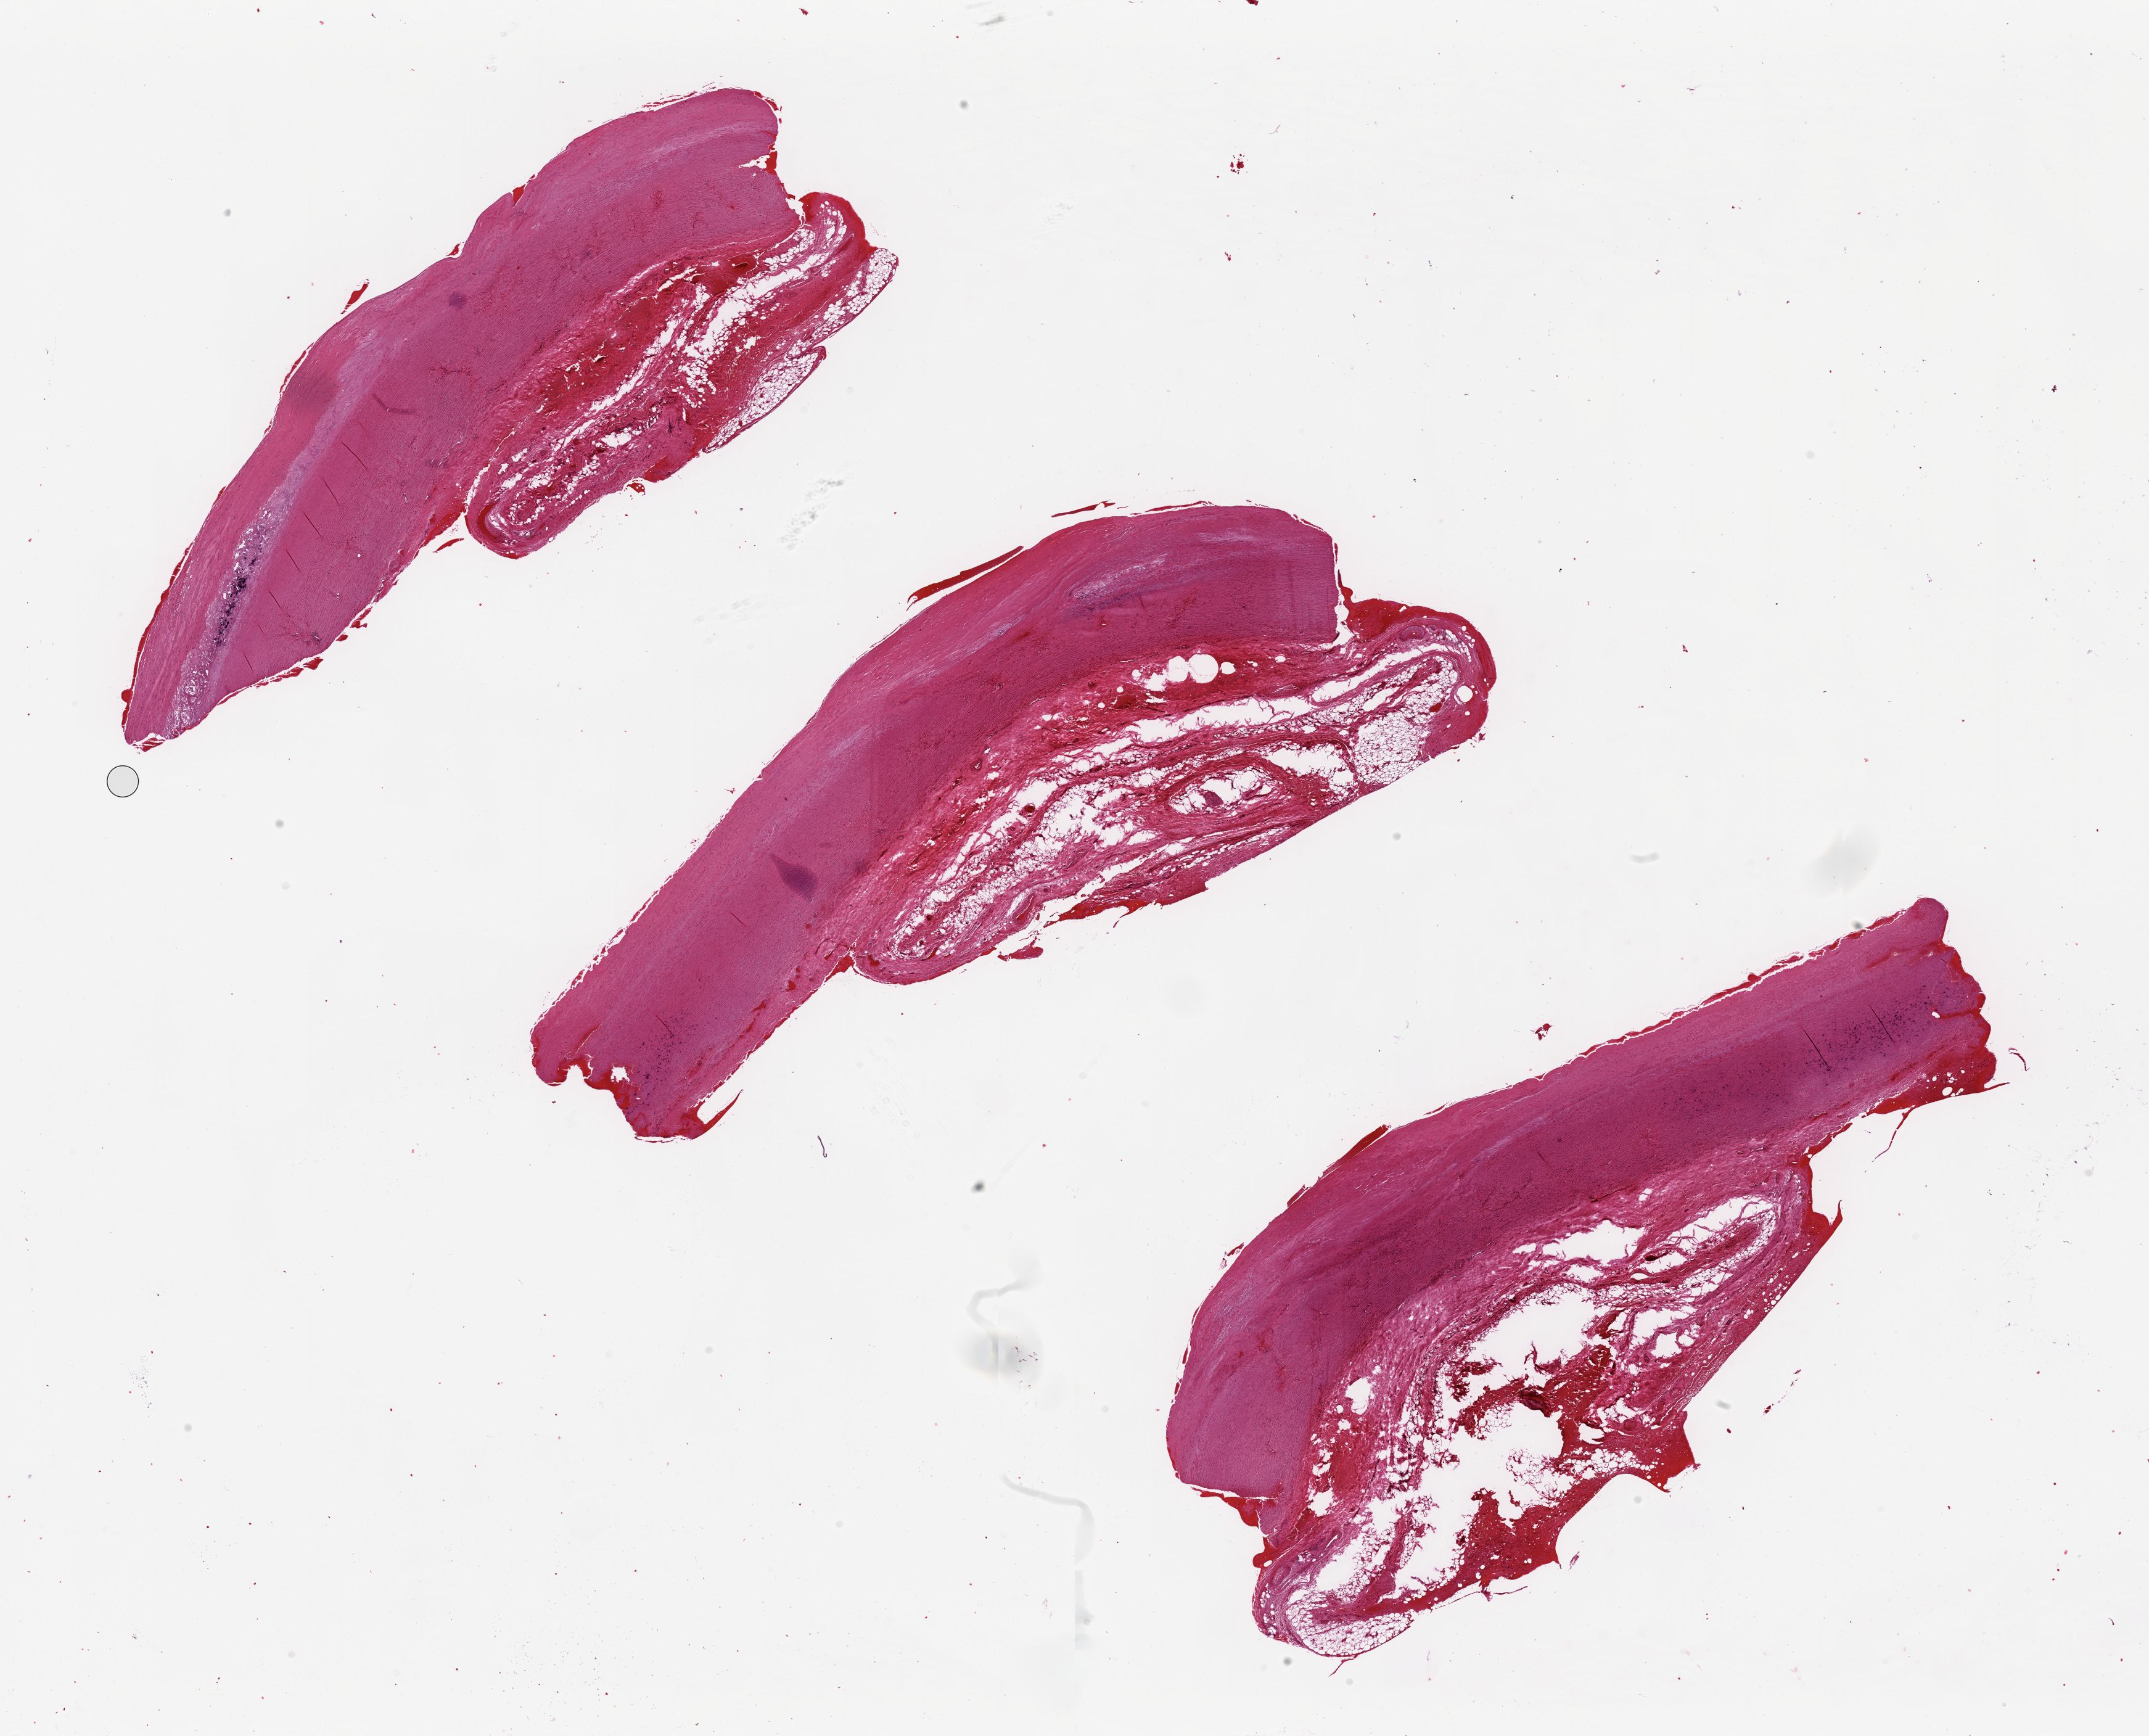
Haematoxylin and eosin whole-slide image, brightfield, shown as a low-resolution overview of the whole scanned area (about 27.6 x 22.3 mm), PAXgene-fixed paraffin-embedded (PFPE) section, sampled site (target tissue): aorta, tissue donor sample.
Review note (as recorded): Fibrocalcific fatty plaque.